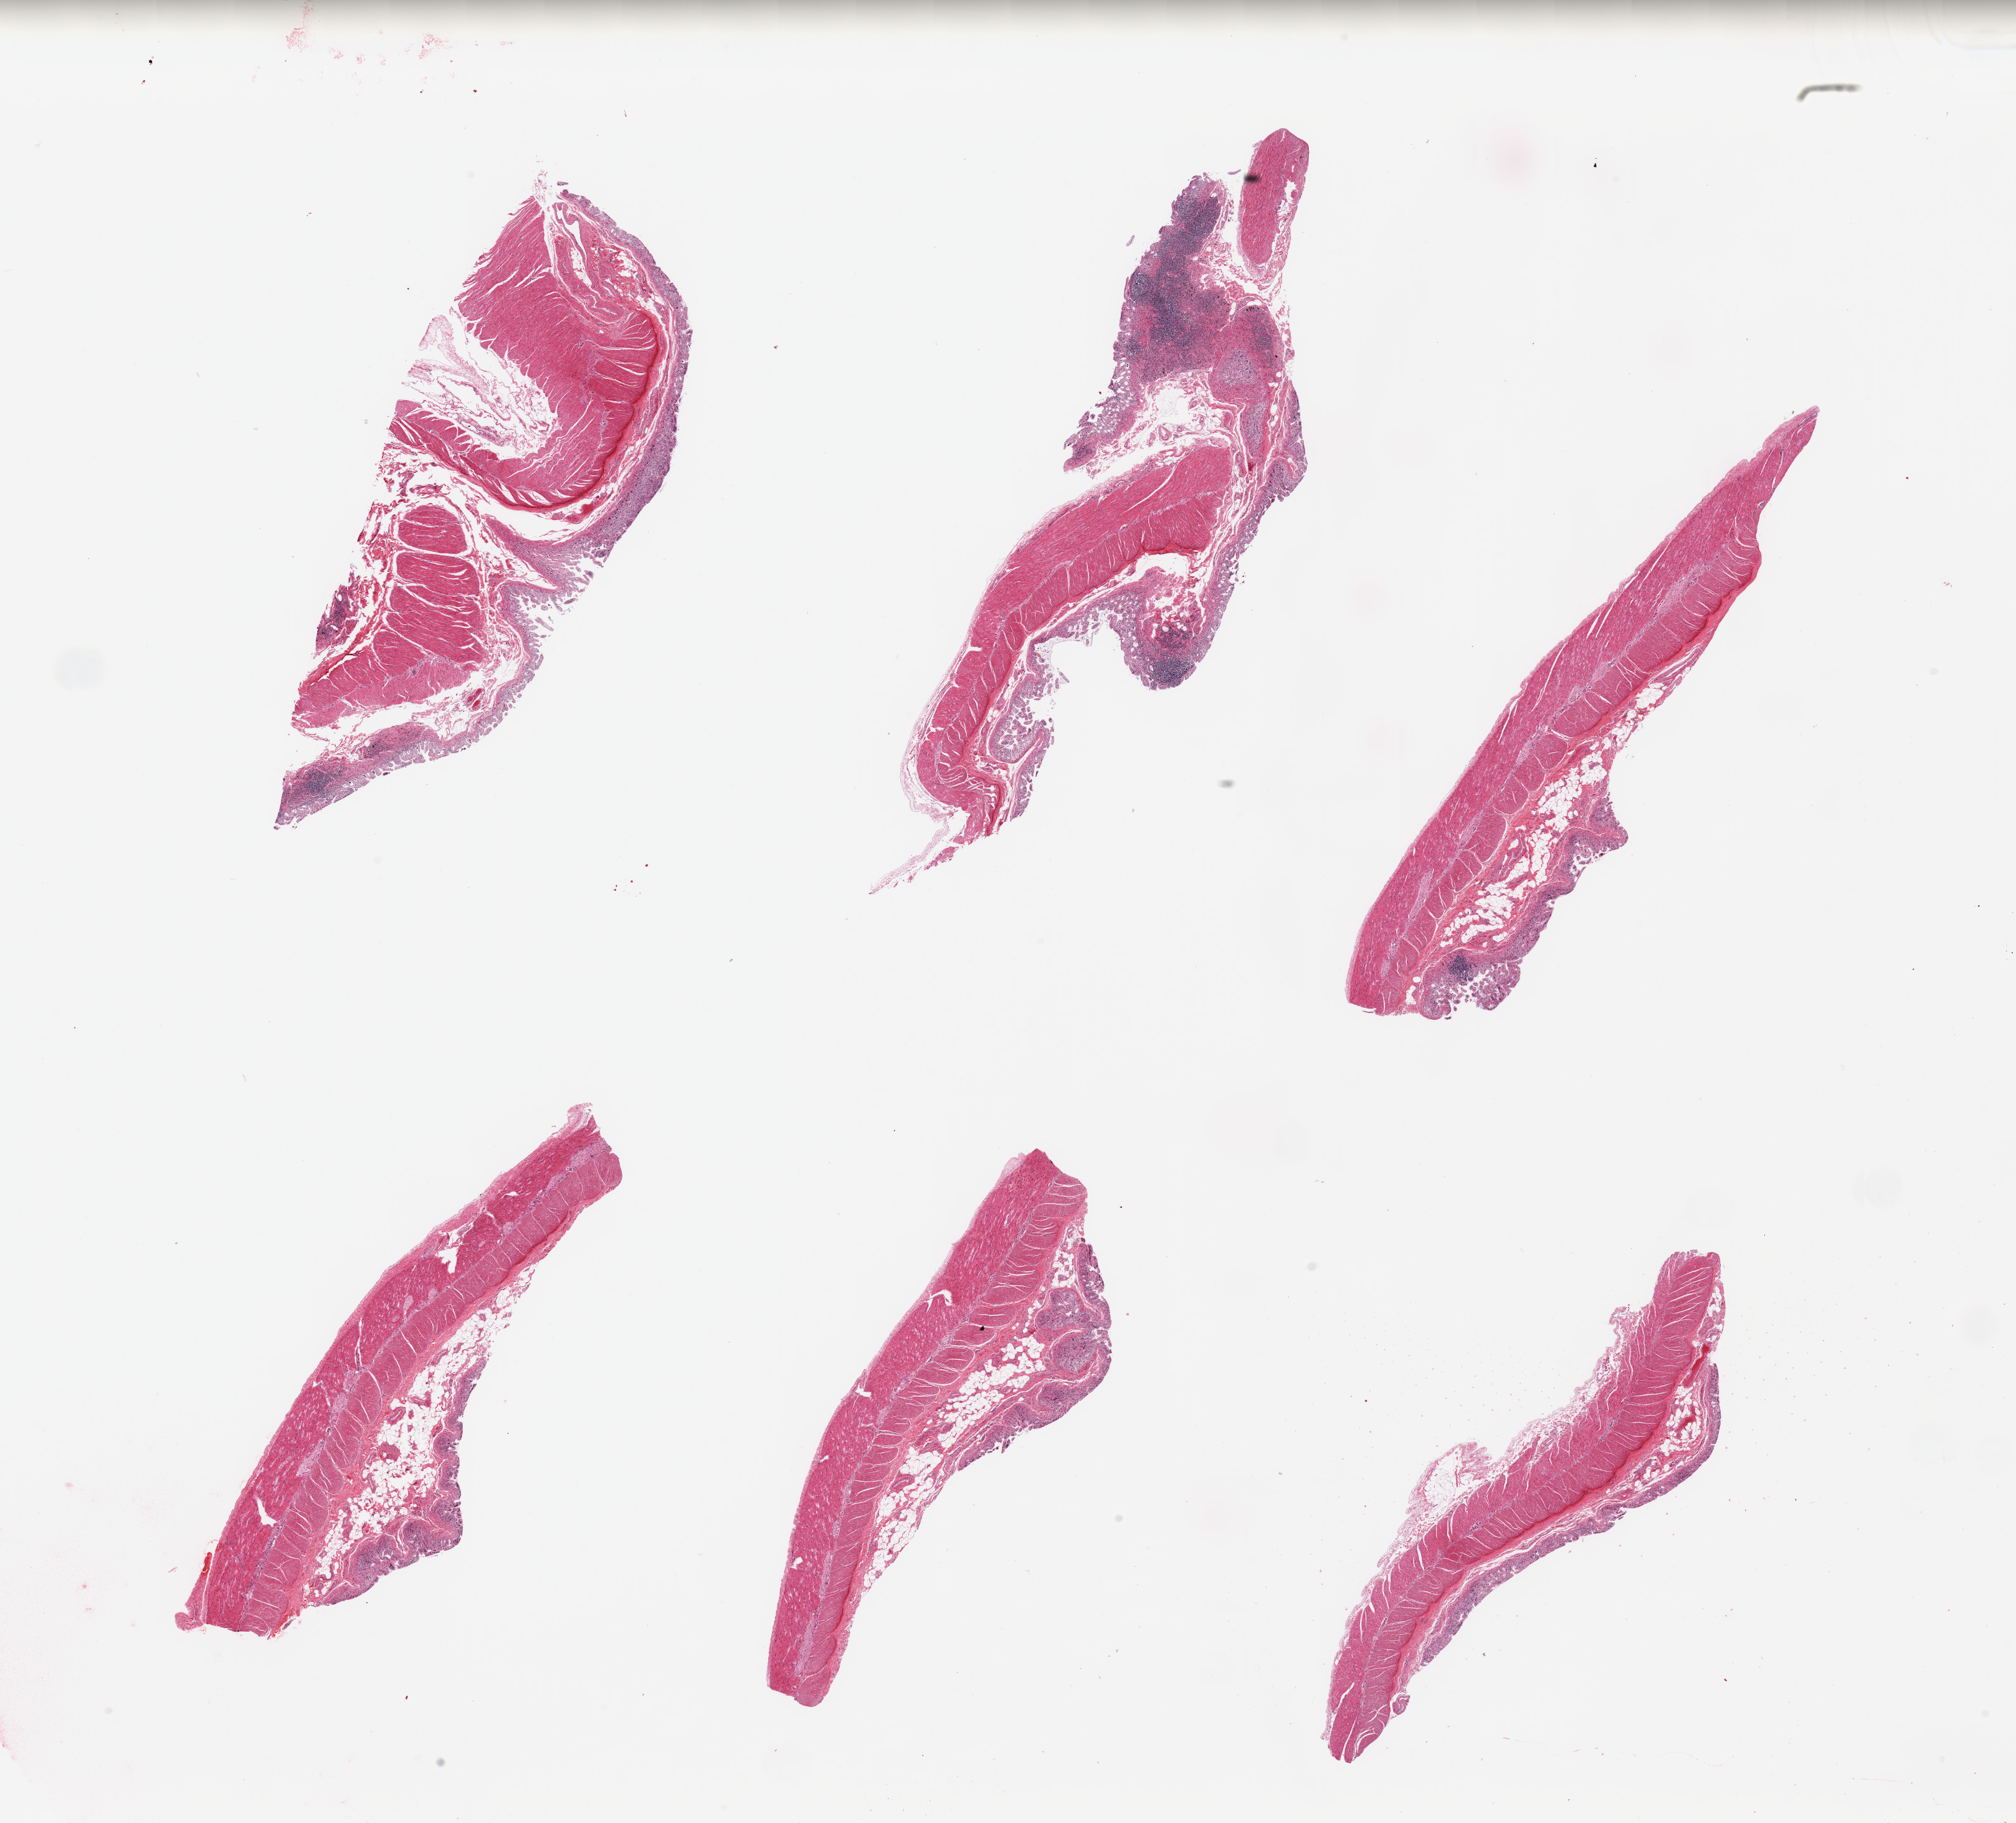
Whole-slide image, hematoxylin and eosin (H&E) stain — low-resolution overview of the scanned area, about 25.6 x 23.1 mm (slide scanned at 20x); PAXgene-fixed paraffin-embedded (PFPE) section; section of ileum (target tissue); tissue donor sample. Donor: female.
- pathologist's review note for this sample: 6 pieces, advanced mucosal glandular autolysis; target lymphoid aggregates are ~10% of tissue